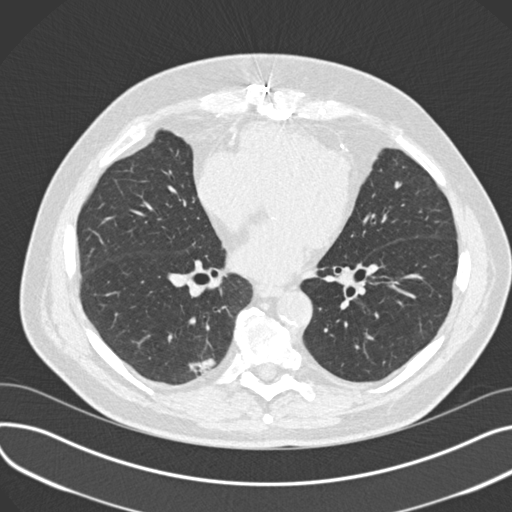
Axial slice from a low-dose chest CT screening exam, third screening round (two years after baseline), lung window (W 1500 / L -600 HU), standard (soft-tissue) reconstruction kernel (B30f), slice 100 of 177 in the series, 512 × 512 image matrix. Male participant, aged 68 years at enrolment. Former smoker at enrolment.
- Lesion marked by an expert reader, bounding box [x1, y1, x2, y2] px = [178, 347, 223, 388].
- The screening reader recorded 4 non-calcified nodules or masses ≥4 mm on this exam; which of them this box marks is not recorded.
- Later outcome: lung cancer diagnosed 68 days after this screen — adenosquamous carcinoma, right lower lobe, moderately differentiated (G2), stage IB (AJCC 6th edition), 31 mm at pathology.